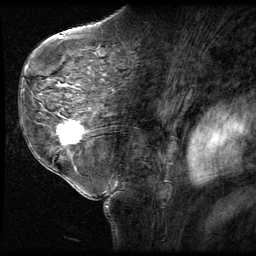
Breast MRI (dynamic contrast-enhanced), one sagittal slice. 3 images stored at this slice position (order not interpretable as contrast timing). 1.5 T. TE 4.2 ms, TR 9 ms. 2.5 mm slice thickness. 256 × 256 image matrix, field of view 180 × 180 mm. Female patient, age 58 years. From the clinical record (not read from this slice): setting: breast cancer imaged before/during neoadjuvant chemotherapy; receptor status: HR-positive, HER2-negative.
Outlined on this slice (semi-automatically segmented with operator editing):
- analysis volume of interest (the breast-tissue region the enhancement analysis was run in; not a lesion): bounding box [x1, y1, x2, y2] px = [51, 116, 93, 151]
- tumour enhancement mask (voxels above the 140 % enhancement threshold inside the analysis volume of interest): [58, 120, 85, 143]